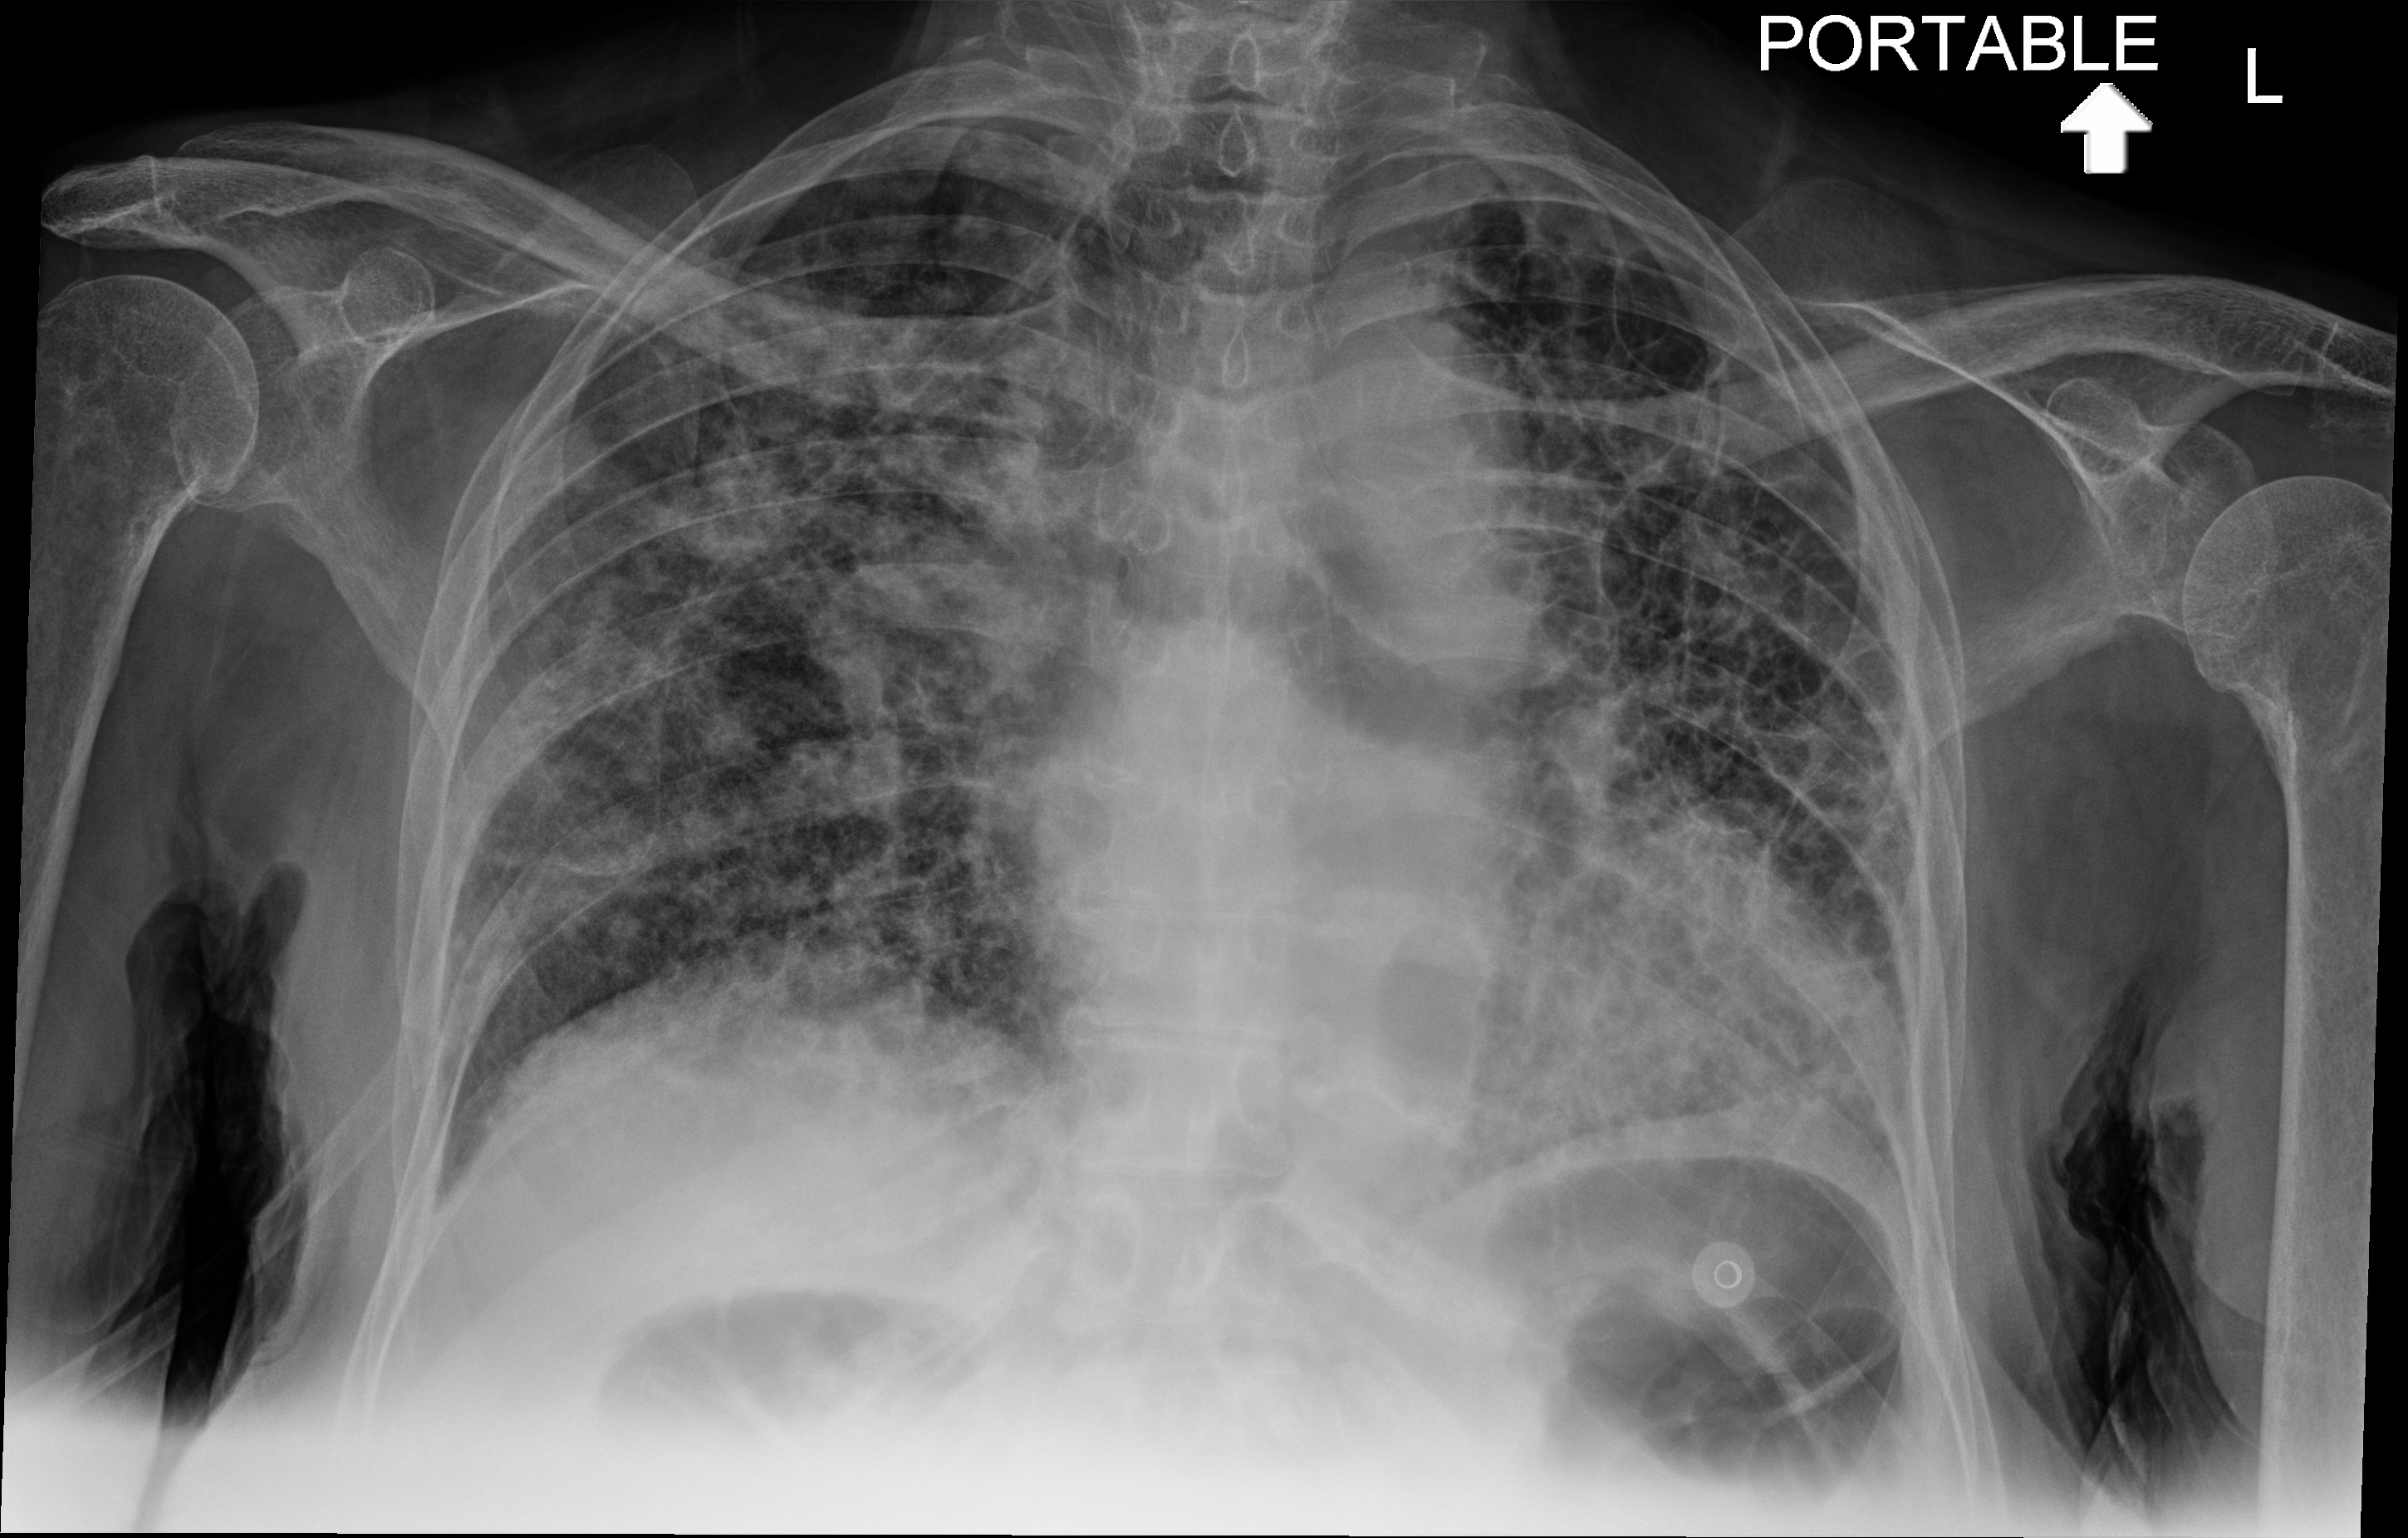
Chest X-ray. Patient hospitalised with COVID-19; female, aged 60–74 years.
Hospital-stay facts (about this admission, not read from this image; timing relative to this image not recorded):
- mechanically ventilated during this hospital stay: no
- admitted to intensive care during this hospital stay: no
- length of hospital stay: 12 days